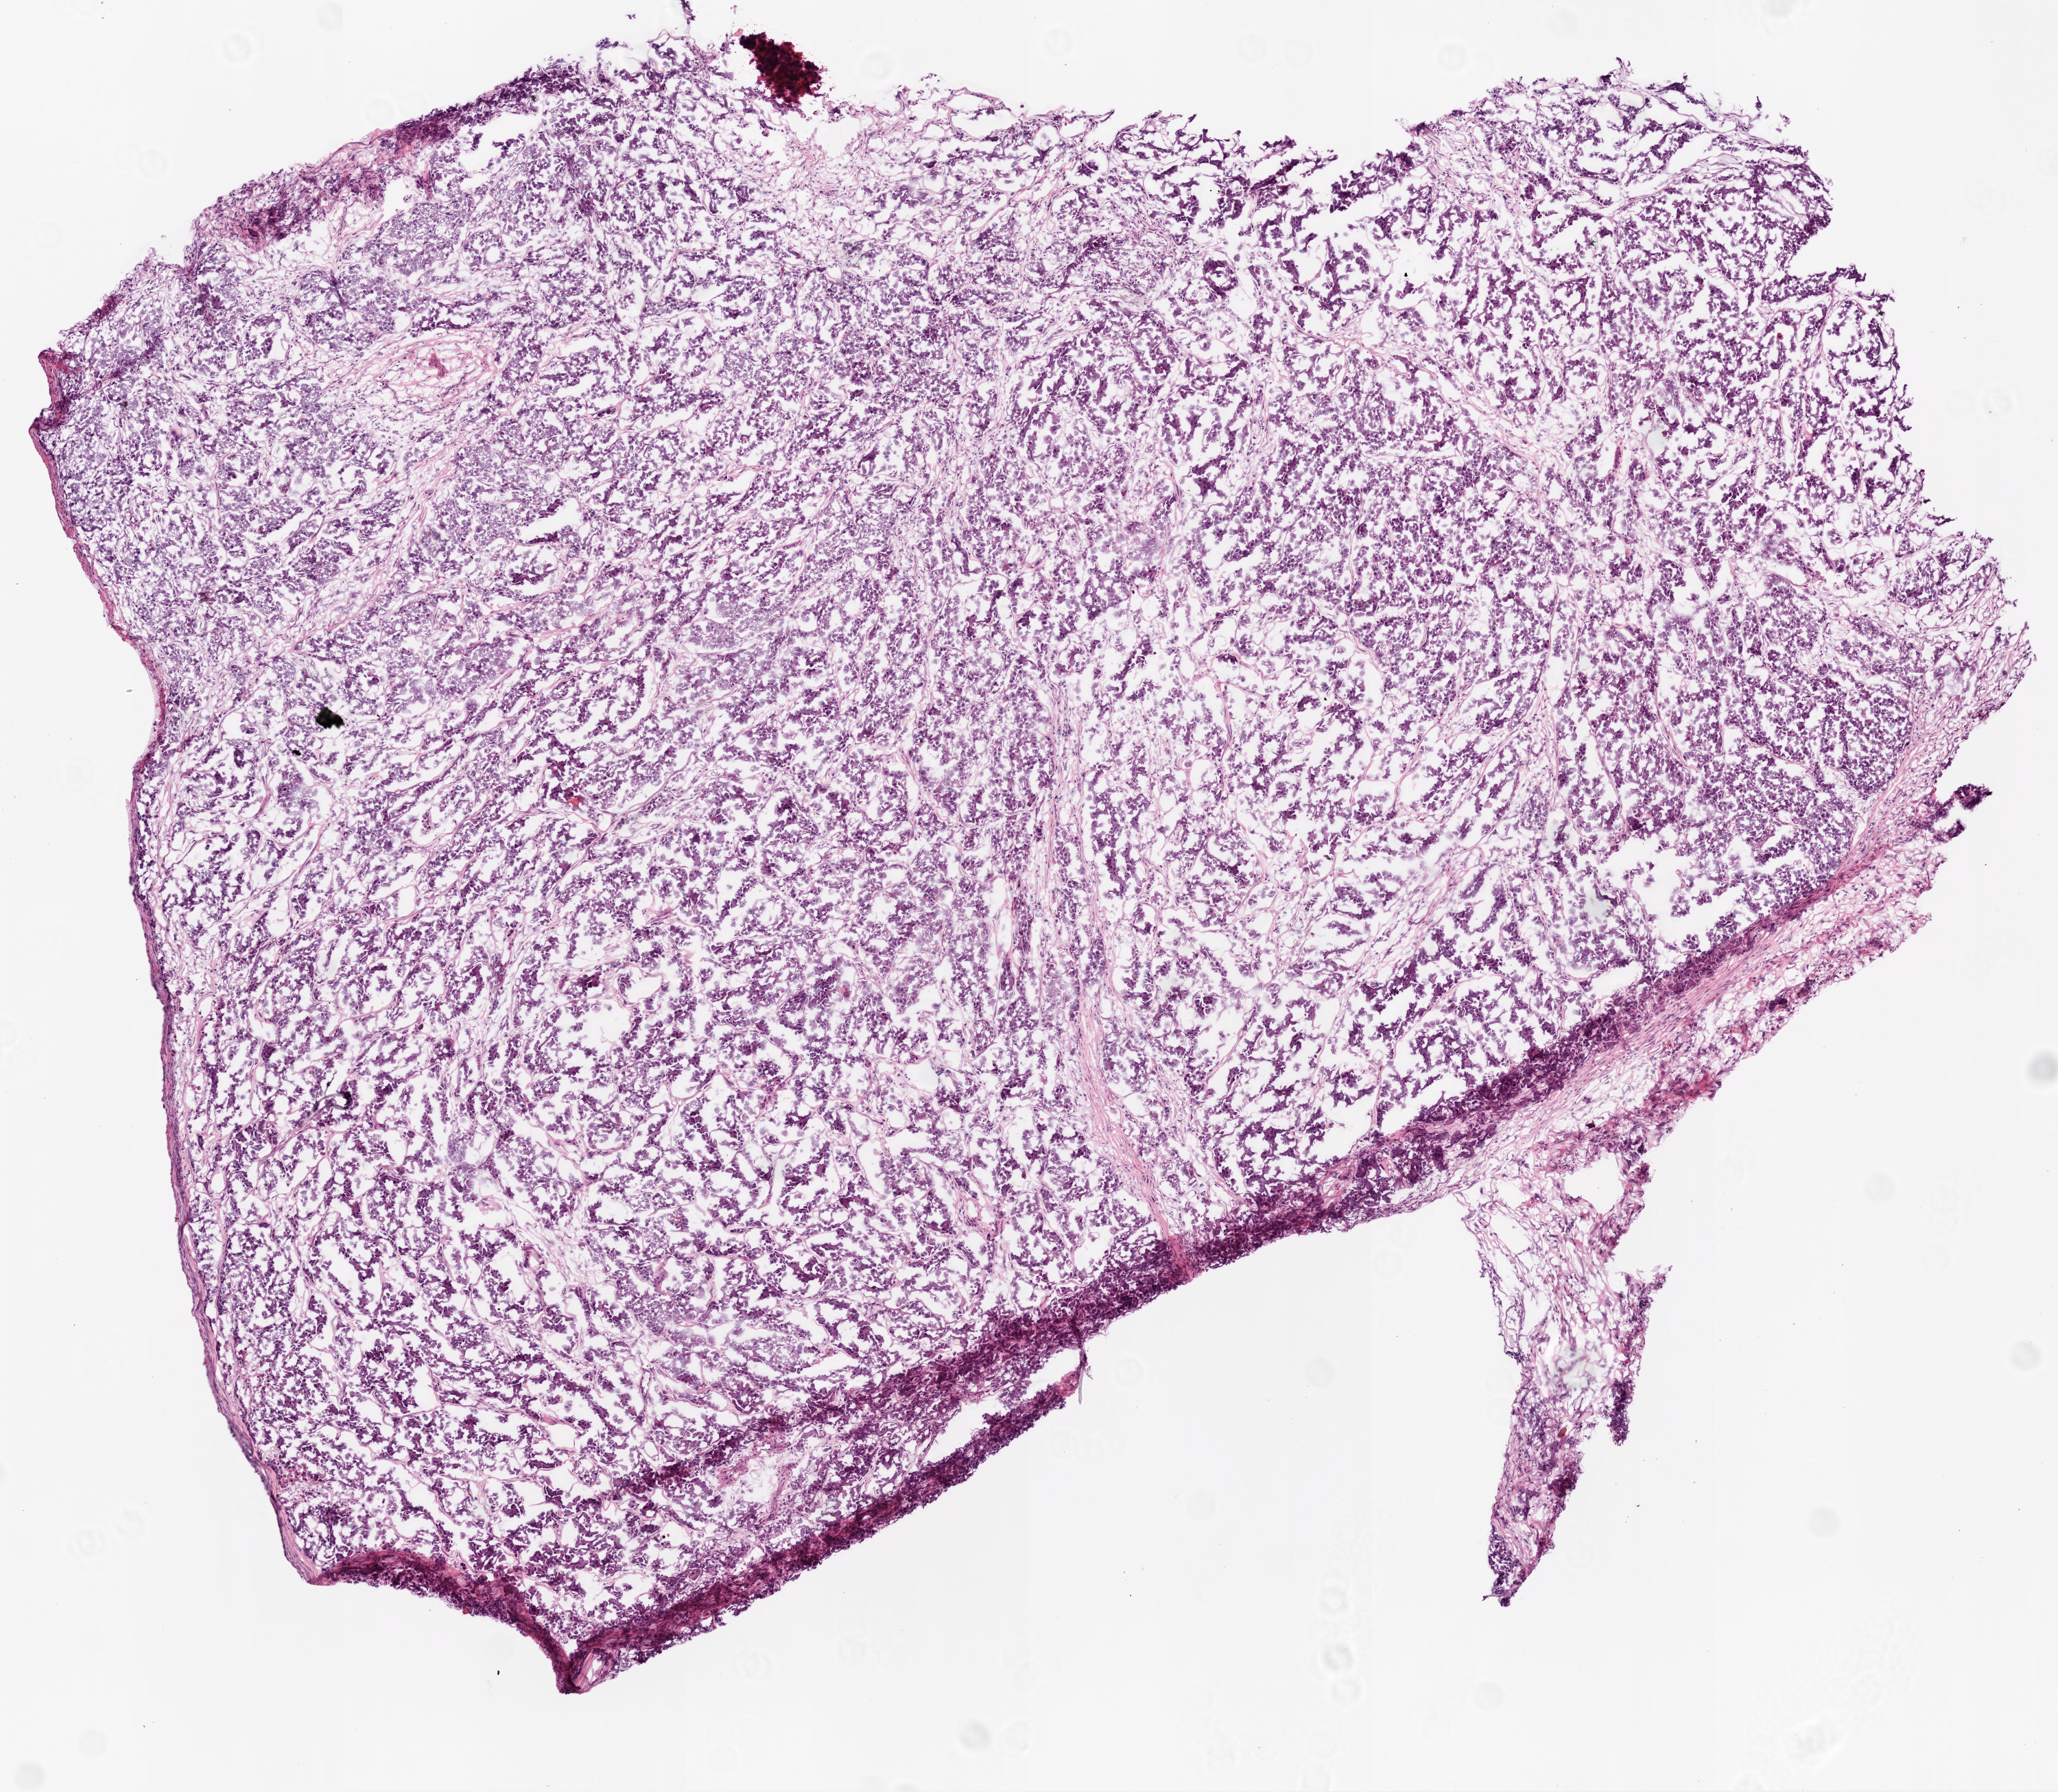
Whole-slide histology image, H&E-stained, whole scanned area (about 6.0 x 5.2 mm) shown as a low-resolution overview. Frozen section from the top of the tissue portion. Primary tumour sample from the ovary. Female patient; age at initial diagnosis 50 years. Histologic grade: G3 (poorly differentiated). Slide review estimates, as recorded: tumour cells 90%, tumour nuclei 90%, normal cells 0%, stromal cells 10%, necrosis 0%.
FIGO stage: IIIC. Histologic diagnosis: Serous cystadenocarcinoma, NOS.